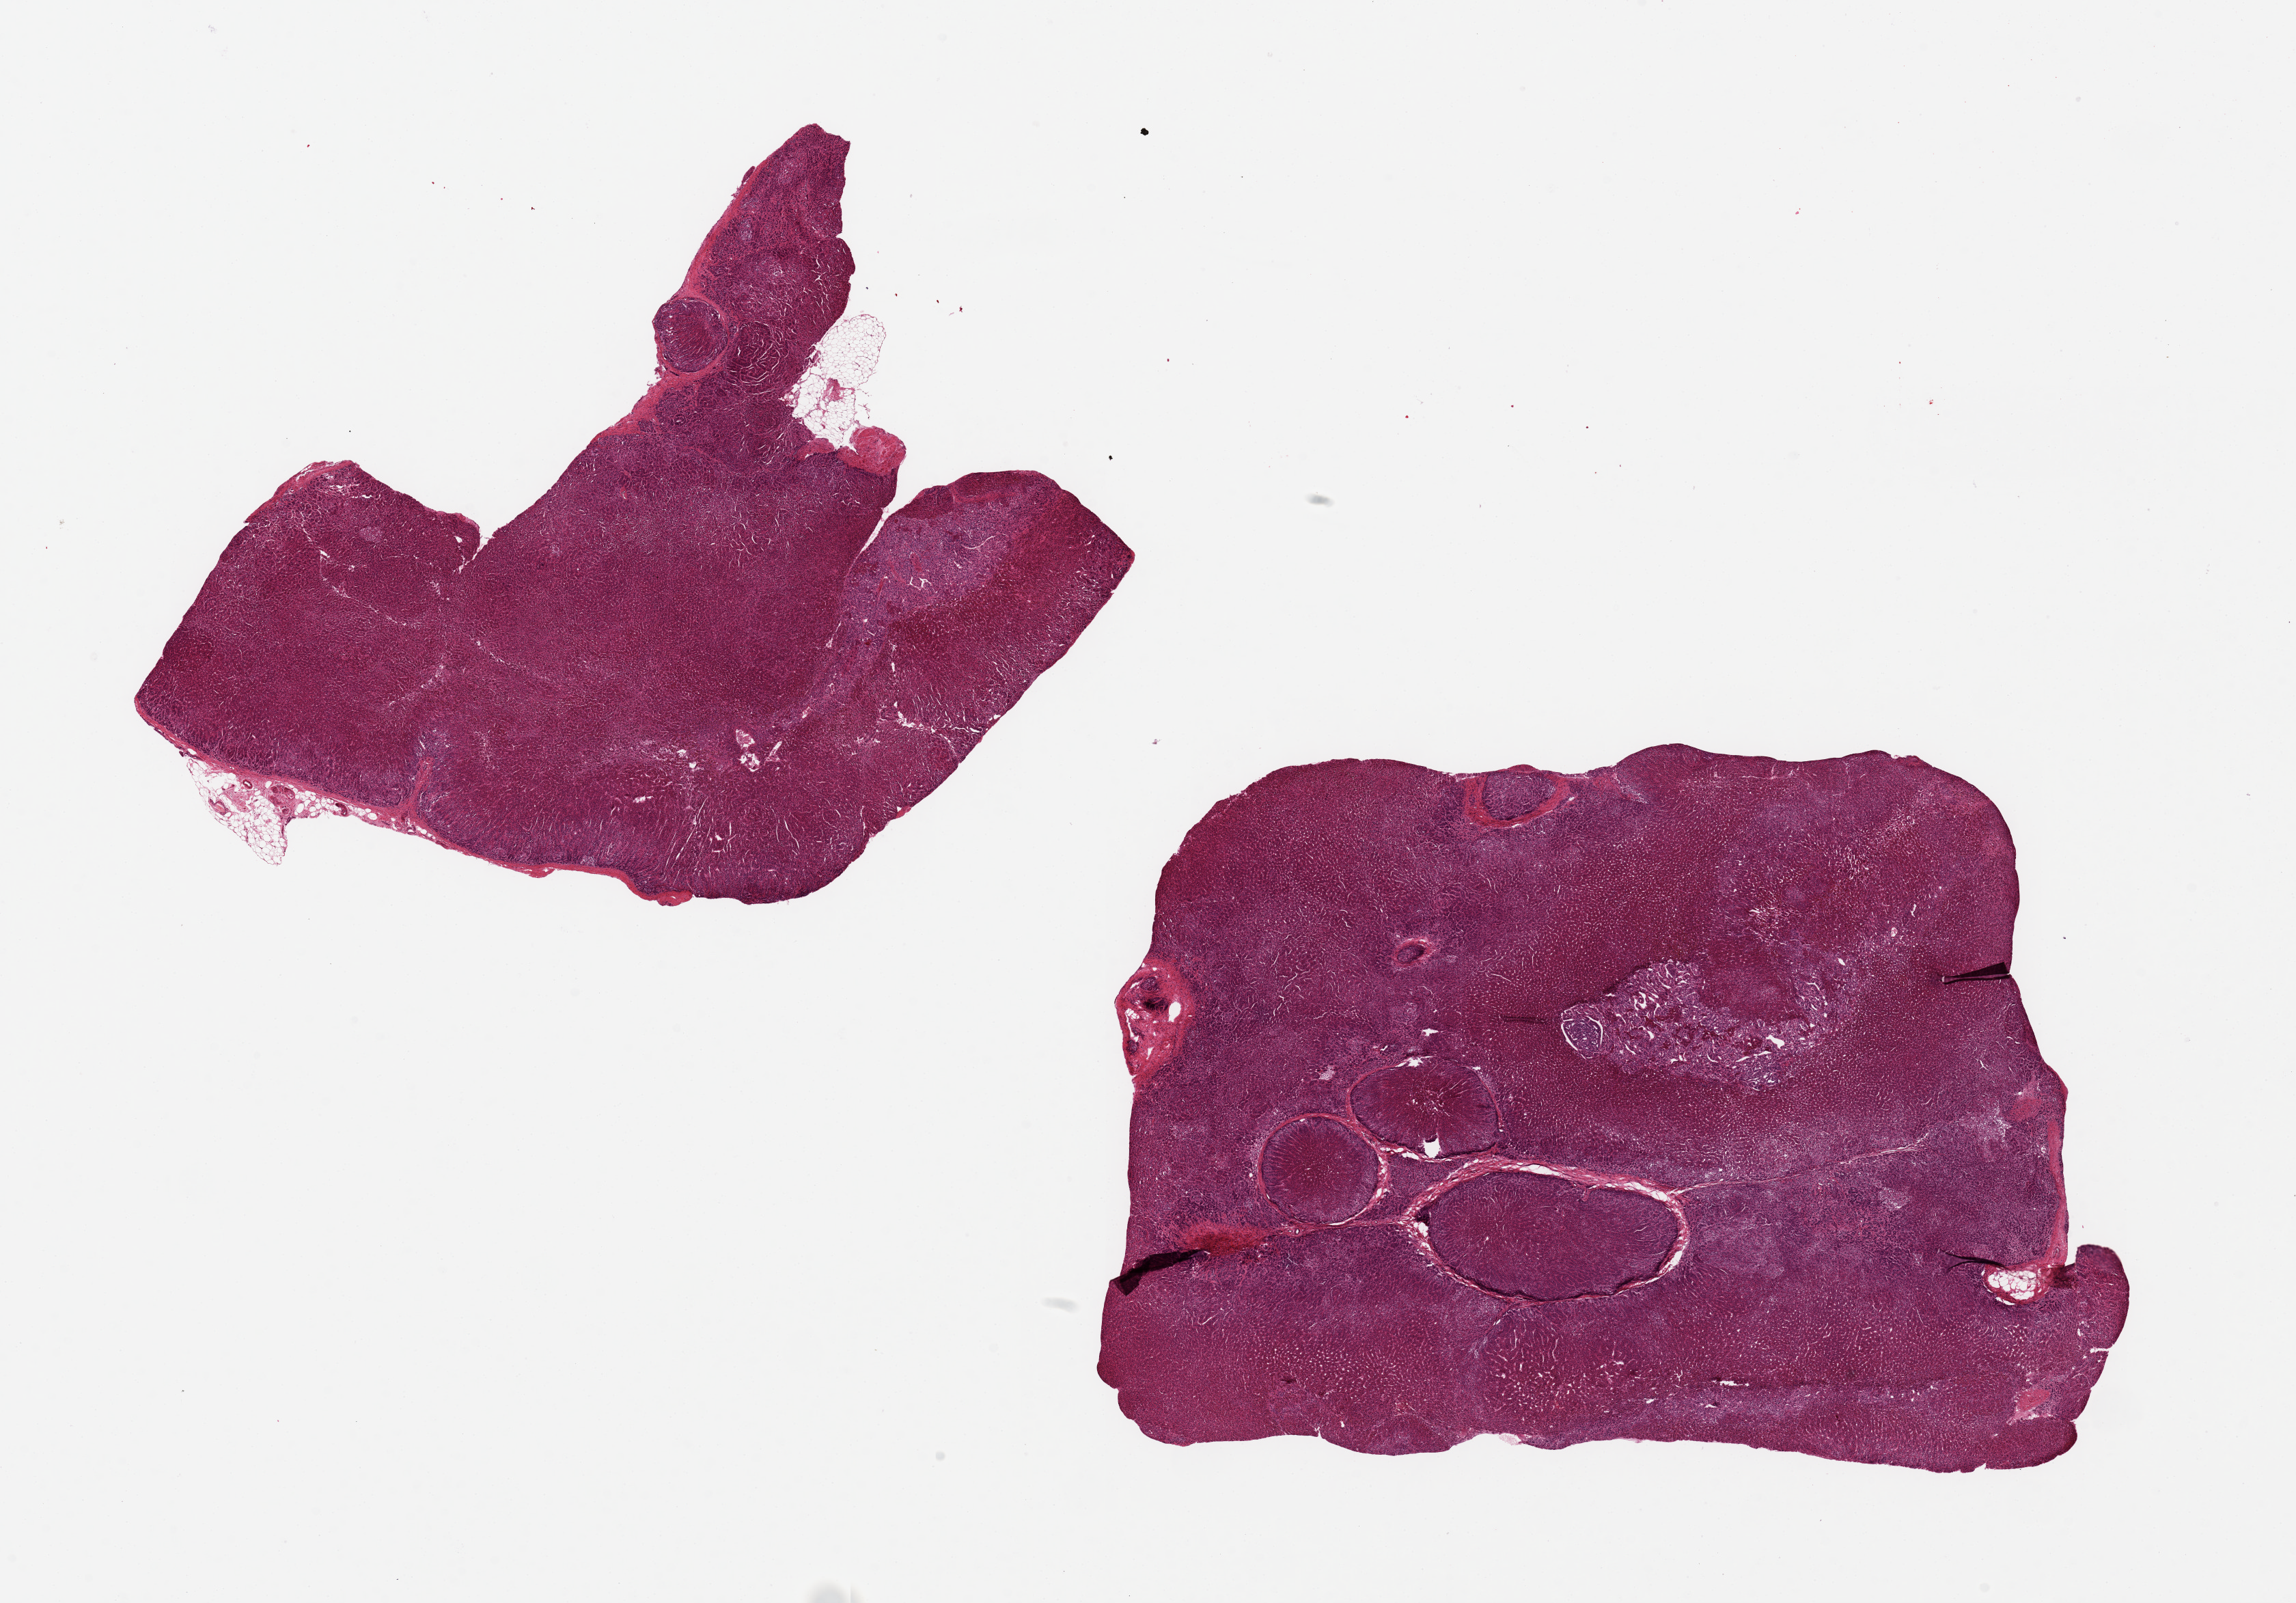
Digitized haematoxylin and eosin-stained section — shown as a low-resolution overview of the whole scanned area (about 26.6 x 18.6 mm, from a 20x scan); PAXgene-fixed paraffin-embedded (PFPE) section; section of adrenal gland (target tissue); donor tissue sample.
Pathologist's review note for this sample: 2 pieces ~10x8mm; ~2mm focus of medulla, reasonably well preserved.